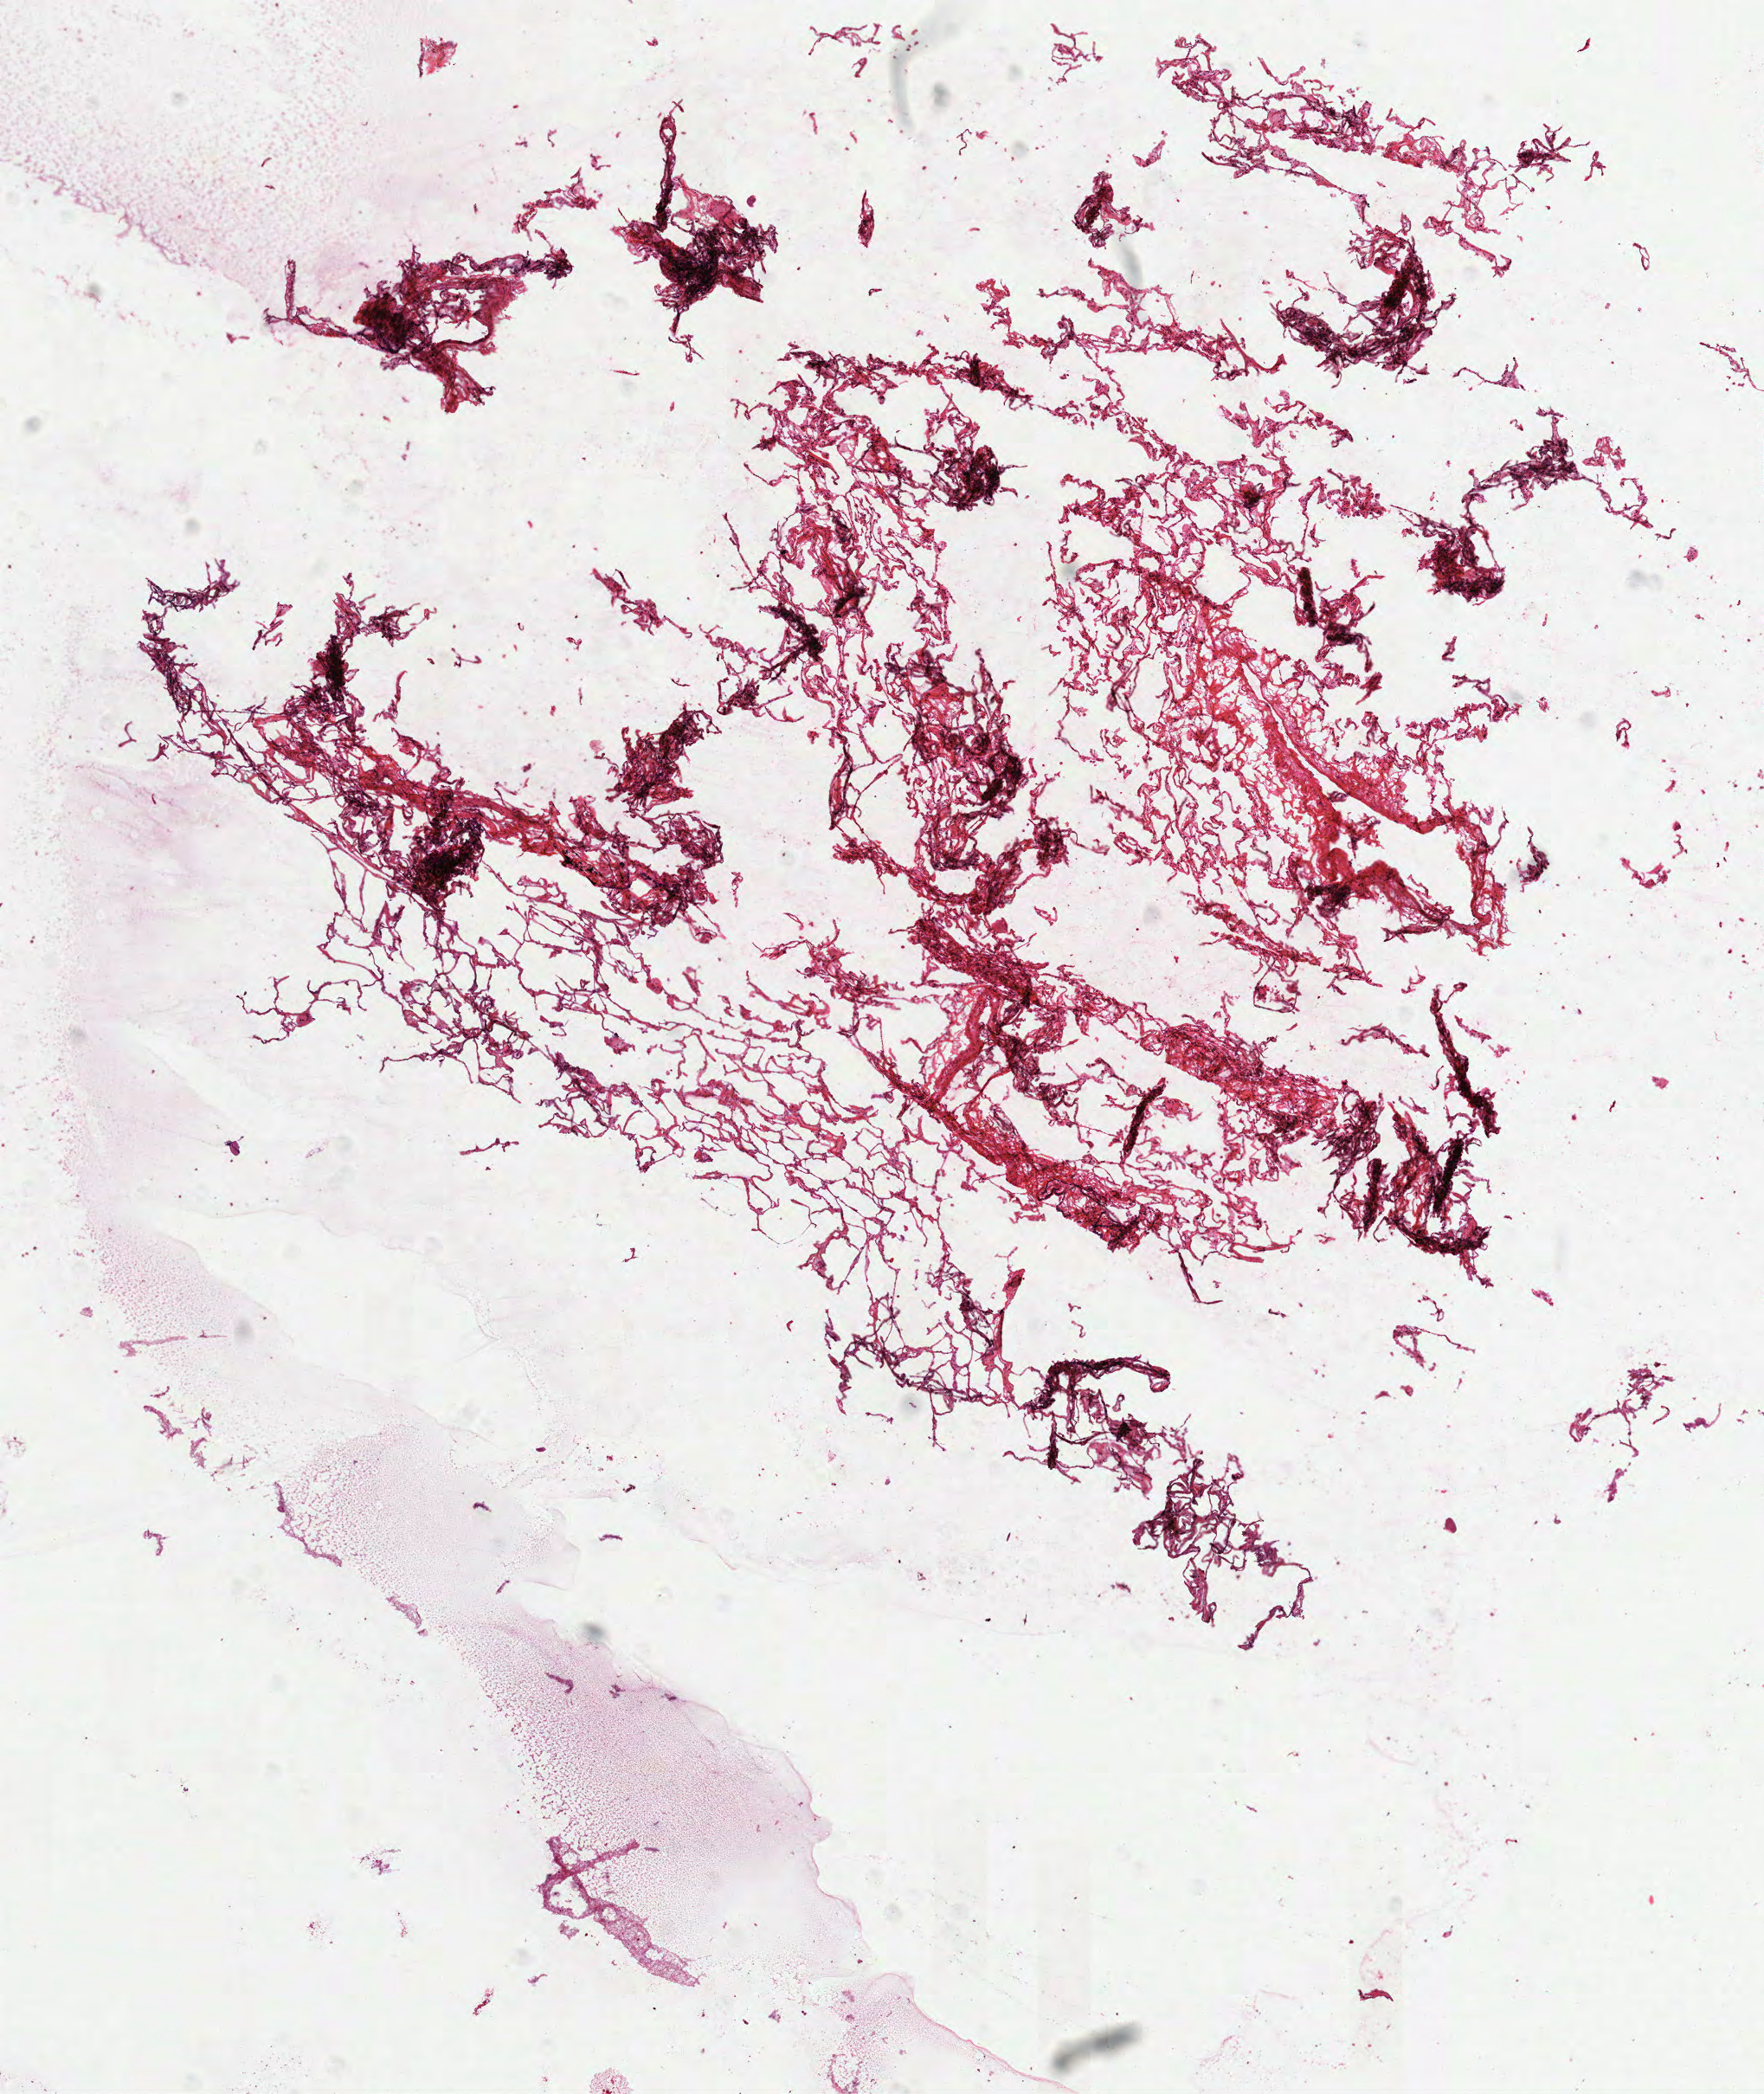
Digitized Hematoxylin and eosin (H&E) stained tissue section (whole slide), whole scanned area (about 8.2 x 9.8 mm, slide scanned at 40x) shown as a low-resolution overview. Frozen section from the top of the tissue portion. Solid tissue normal (non-tumour tissue) sample from the lung. Patient: male, age at initial diagnosis 74 years.
- this section: solid tissue normal (non-tumour) sample from the same patient
- patient diagnosis: Papillary adenocarcinoma, NOS (upper lobe, lung)